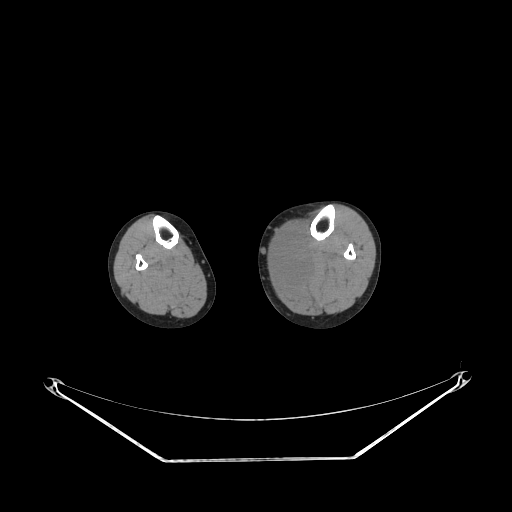
CT of an extremity soft-tissue mass (from a PET/CT study), one axial slice; position 133 of 223 along the scan axis; soft-tissue window (W 400 / L 40 HU); 3.75 mm slice thickness; 512 × 512 image matrix, field of view 500 × 500 mm. Female patient. From the clinical record (not read from this slice): histological type: extraskeletal high grade osteogenic sarcoma; grade: high; site of the primary tumour: left calf.
Outlined on this slice (expert contour drawn on MRI and transferred to this co-registered scan by the dataset authors):
- gross tumour volume (mass): bounding box (x1, y1, x2, y2) in pixels: (276, 235, 309, 280)